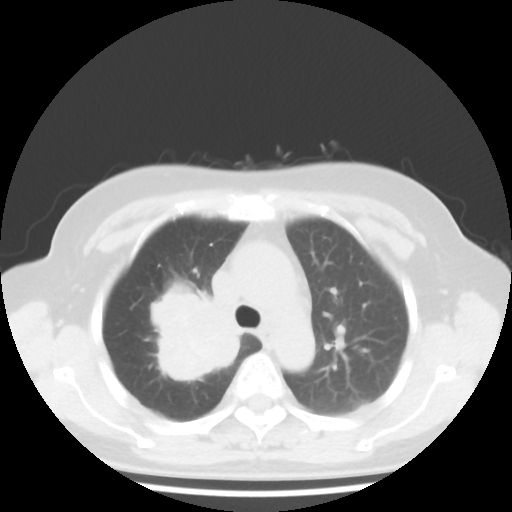
Chest CT, one axial slice; position 30 of 43 along the scan axis; 100 kVp; lung window (W 1500 / L -600 HU); 5 mm slice thickness; 512 × 512 image matrix, field of view 316 × 316 mm. Patient: female, 62 years. From the clinical record (not read from this slice): clinical TNM (as recorded): T3 N0 M0; histopathological grade: G3.
Structures marked on this image (bounding box drawn by a radiologist):
- lung tumour (recorded histology: small cell carcinoma): bounding box <143,285,247,388> (left, top, right, bottom; pixels)